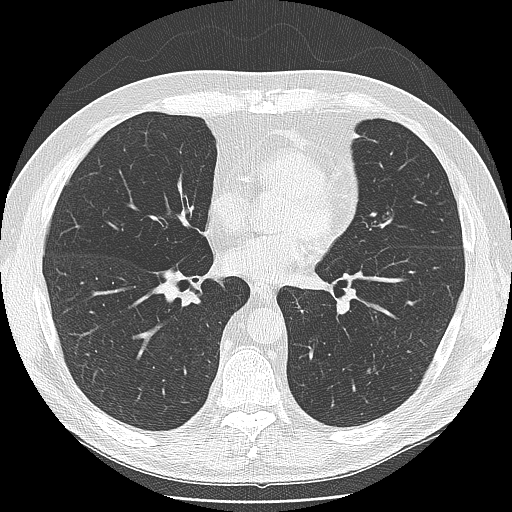
Low-dose screening chest CT, one axial slice; slice 78 of 166 in the series (ordered by position); reconstruction kernel LUNG; 120 kVp; lung window (W 1500 / L -600 HU); 512 × 512 image matrix, field of view 360 × 360 mm.
Structures marked on this image (expert manual segmentation):
- lesion 1 (tumor, lower lobe of left lung): box from (x=367, y=368) to (x=379, y=375) px